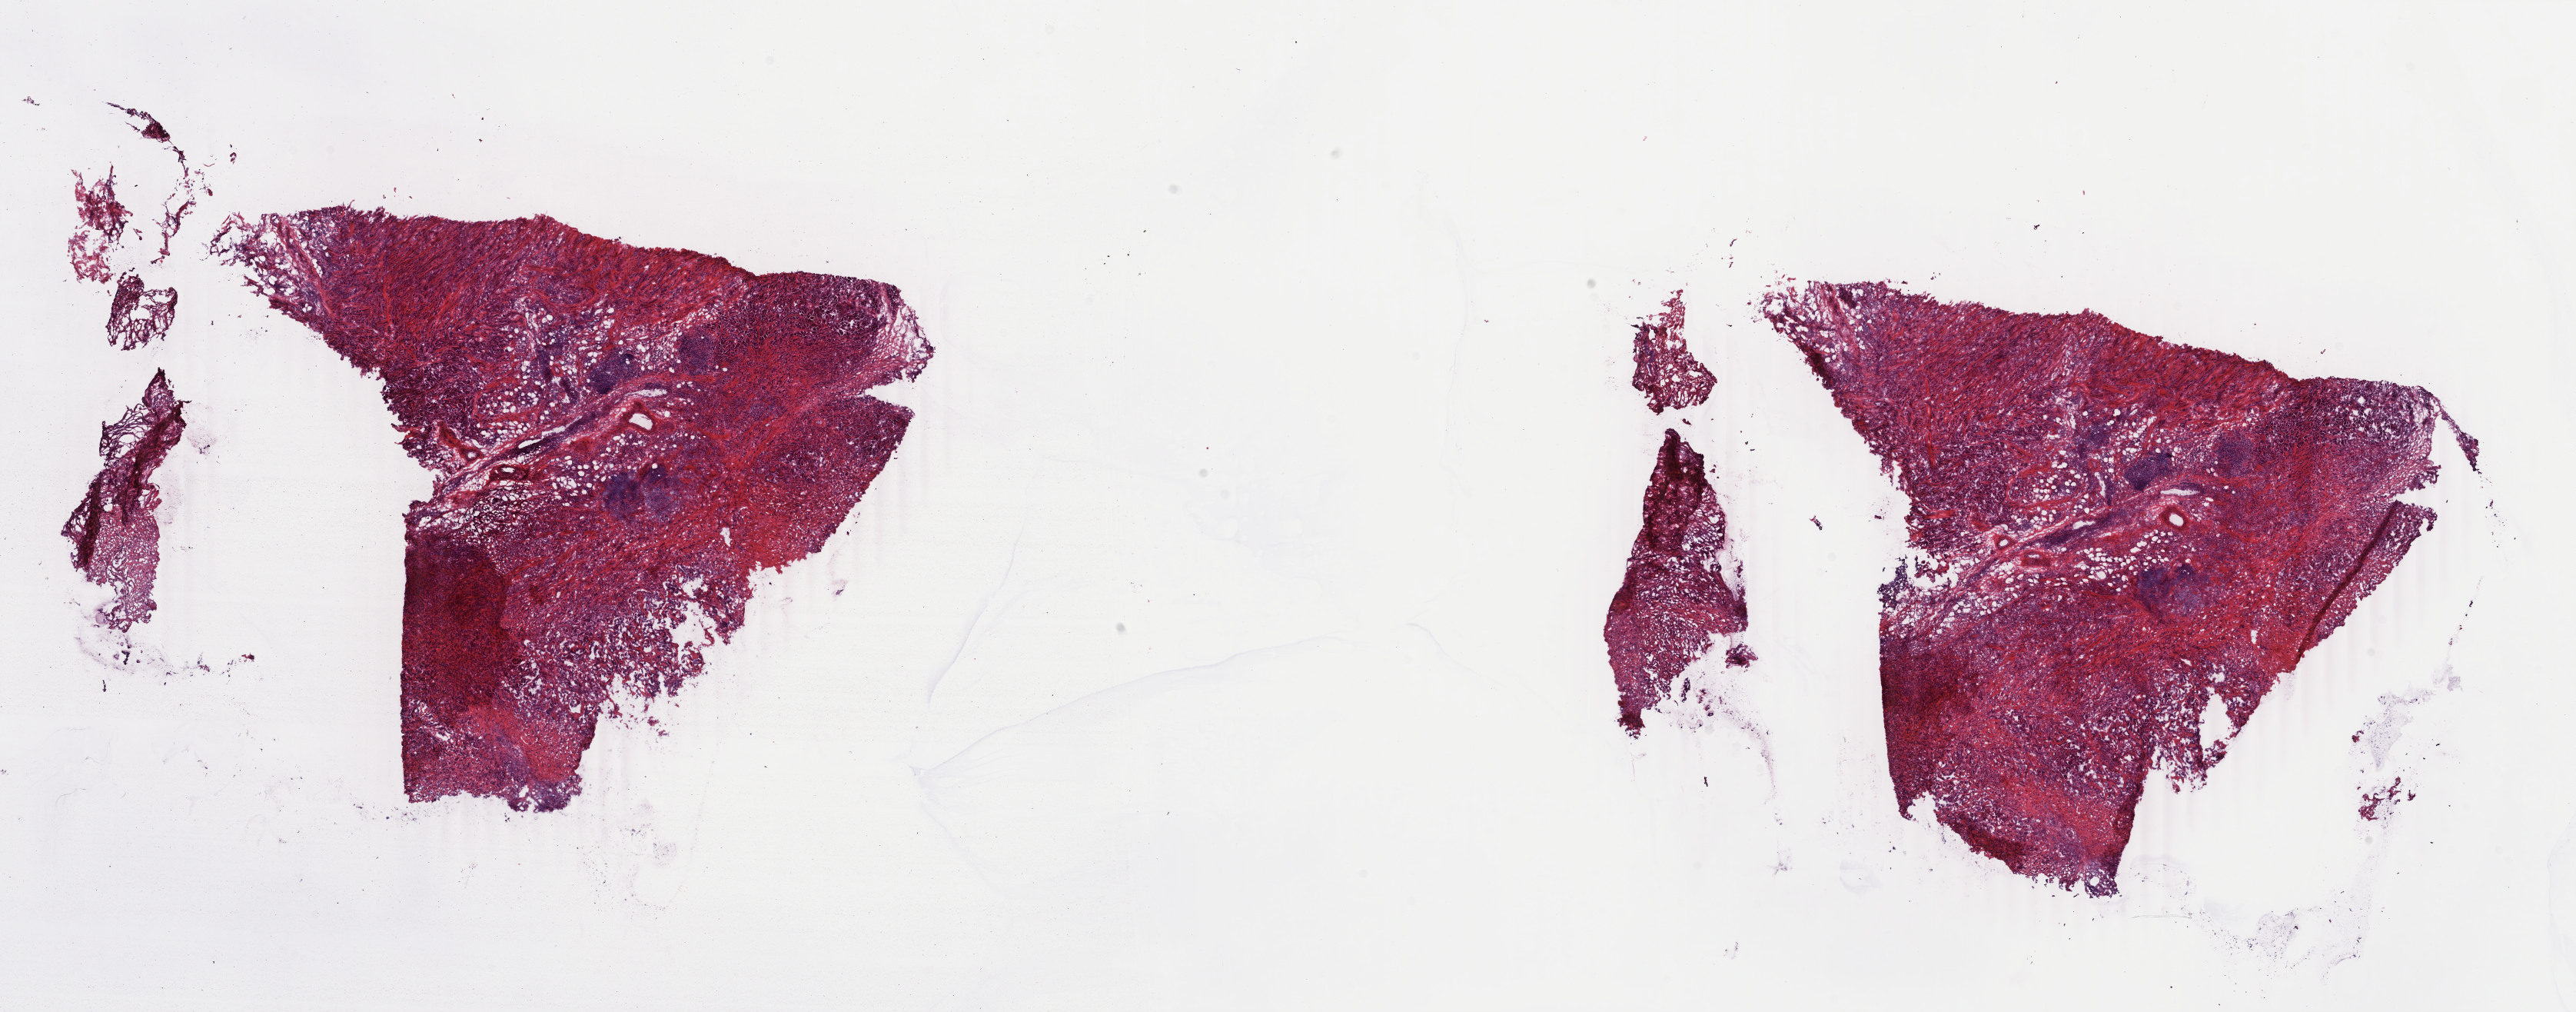
H&E whole-slide image — whole scanned area (about 26.7 x 10.5 mm, slide scanned at 40x) shown as a low-resolution overview; frozen section from the top of the tissue portion; mesothelium, primary tumour sample. Female patient; age at initial diagnosis 60 years. Pathologist review of this section (percent, as recorded): tumour cells 100%, tumour nuclei 70%, normal cells 0%, stromal cells 0%, necrosis 0%. Infiltration values recorded for this section: lymphocyte infiltration 2%, monocyte infiltration 0%, neutrophil infiltration 0%.
• AJCC pathologic stage: II (6th edition)
• TNM: T2 N0 M0
• histologic diagnosis: Epithelioid mesothelioma, malignant (pleura, NOS)